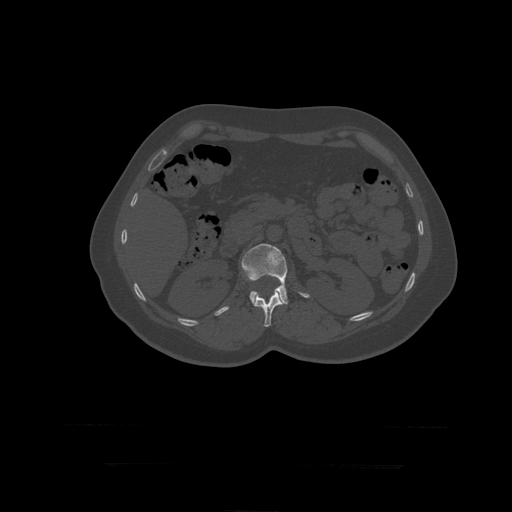
CT including the spine, one axial slice; slice 161 of 399 in the series (ordered by position); 120 kVp; bone window (W 1800 / L 400 HU); 1.25 mm slice thickness; 512 × 512 image matrix. Patient age 41 years. Case-level facts recorded for this patient, not image findings: primary cancer: breast.
Outlined on this slice (semi-automatic segmentation, software-assisted and operator-edited):
- L1 vertebra: bounding box <254,291,284,327> (left, top, right, bottom; pixels)
- L2 vertebra: <242,244,310,305>